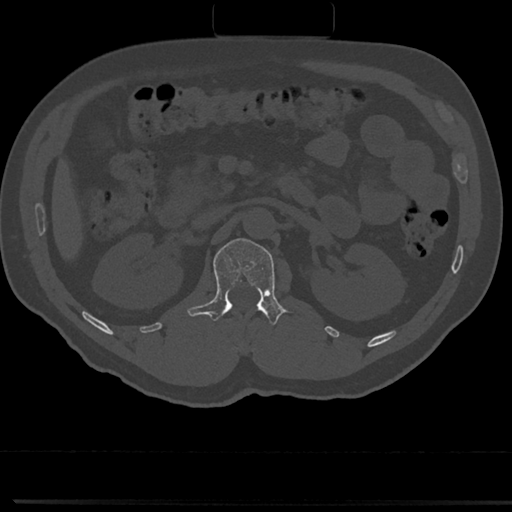
CT including the spine, one axial slice; reconstruction kernel Br40s/3; 120 kVp; bone window (W 1800 / L 400 HU); 0.5 mm slice thickness; 512 × 512 image matrix. Patient: male, 61 years. Case-level facts recorded for this patient, not image findings: primary cancer: prostate.
Annotated regions visible in this slice (semi-automatic segmentation, software-assisted and operator-edited):
- L1 vertebra: box from (x=191, y=239) to (x=287, y=325) px